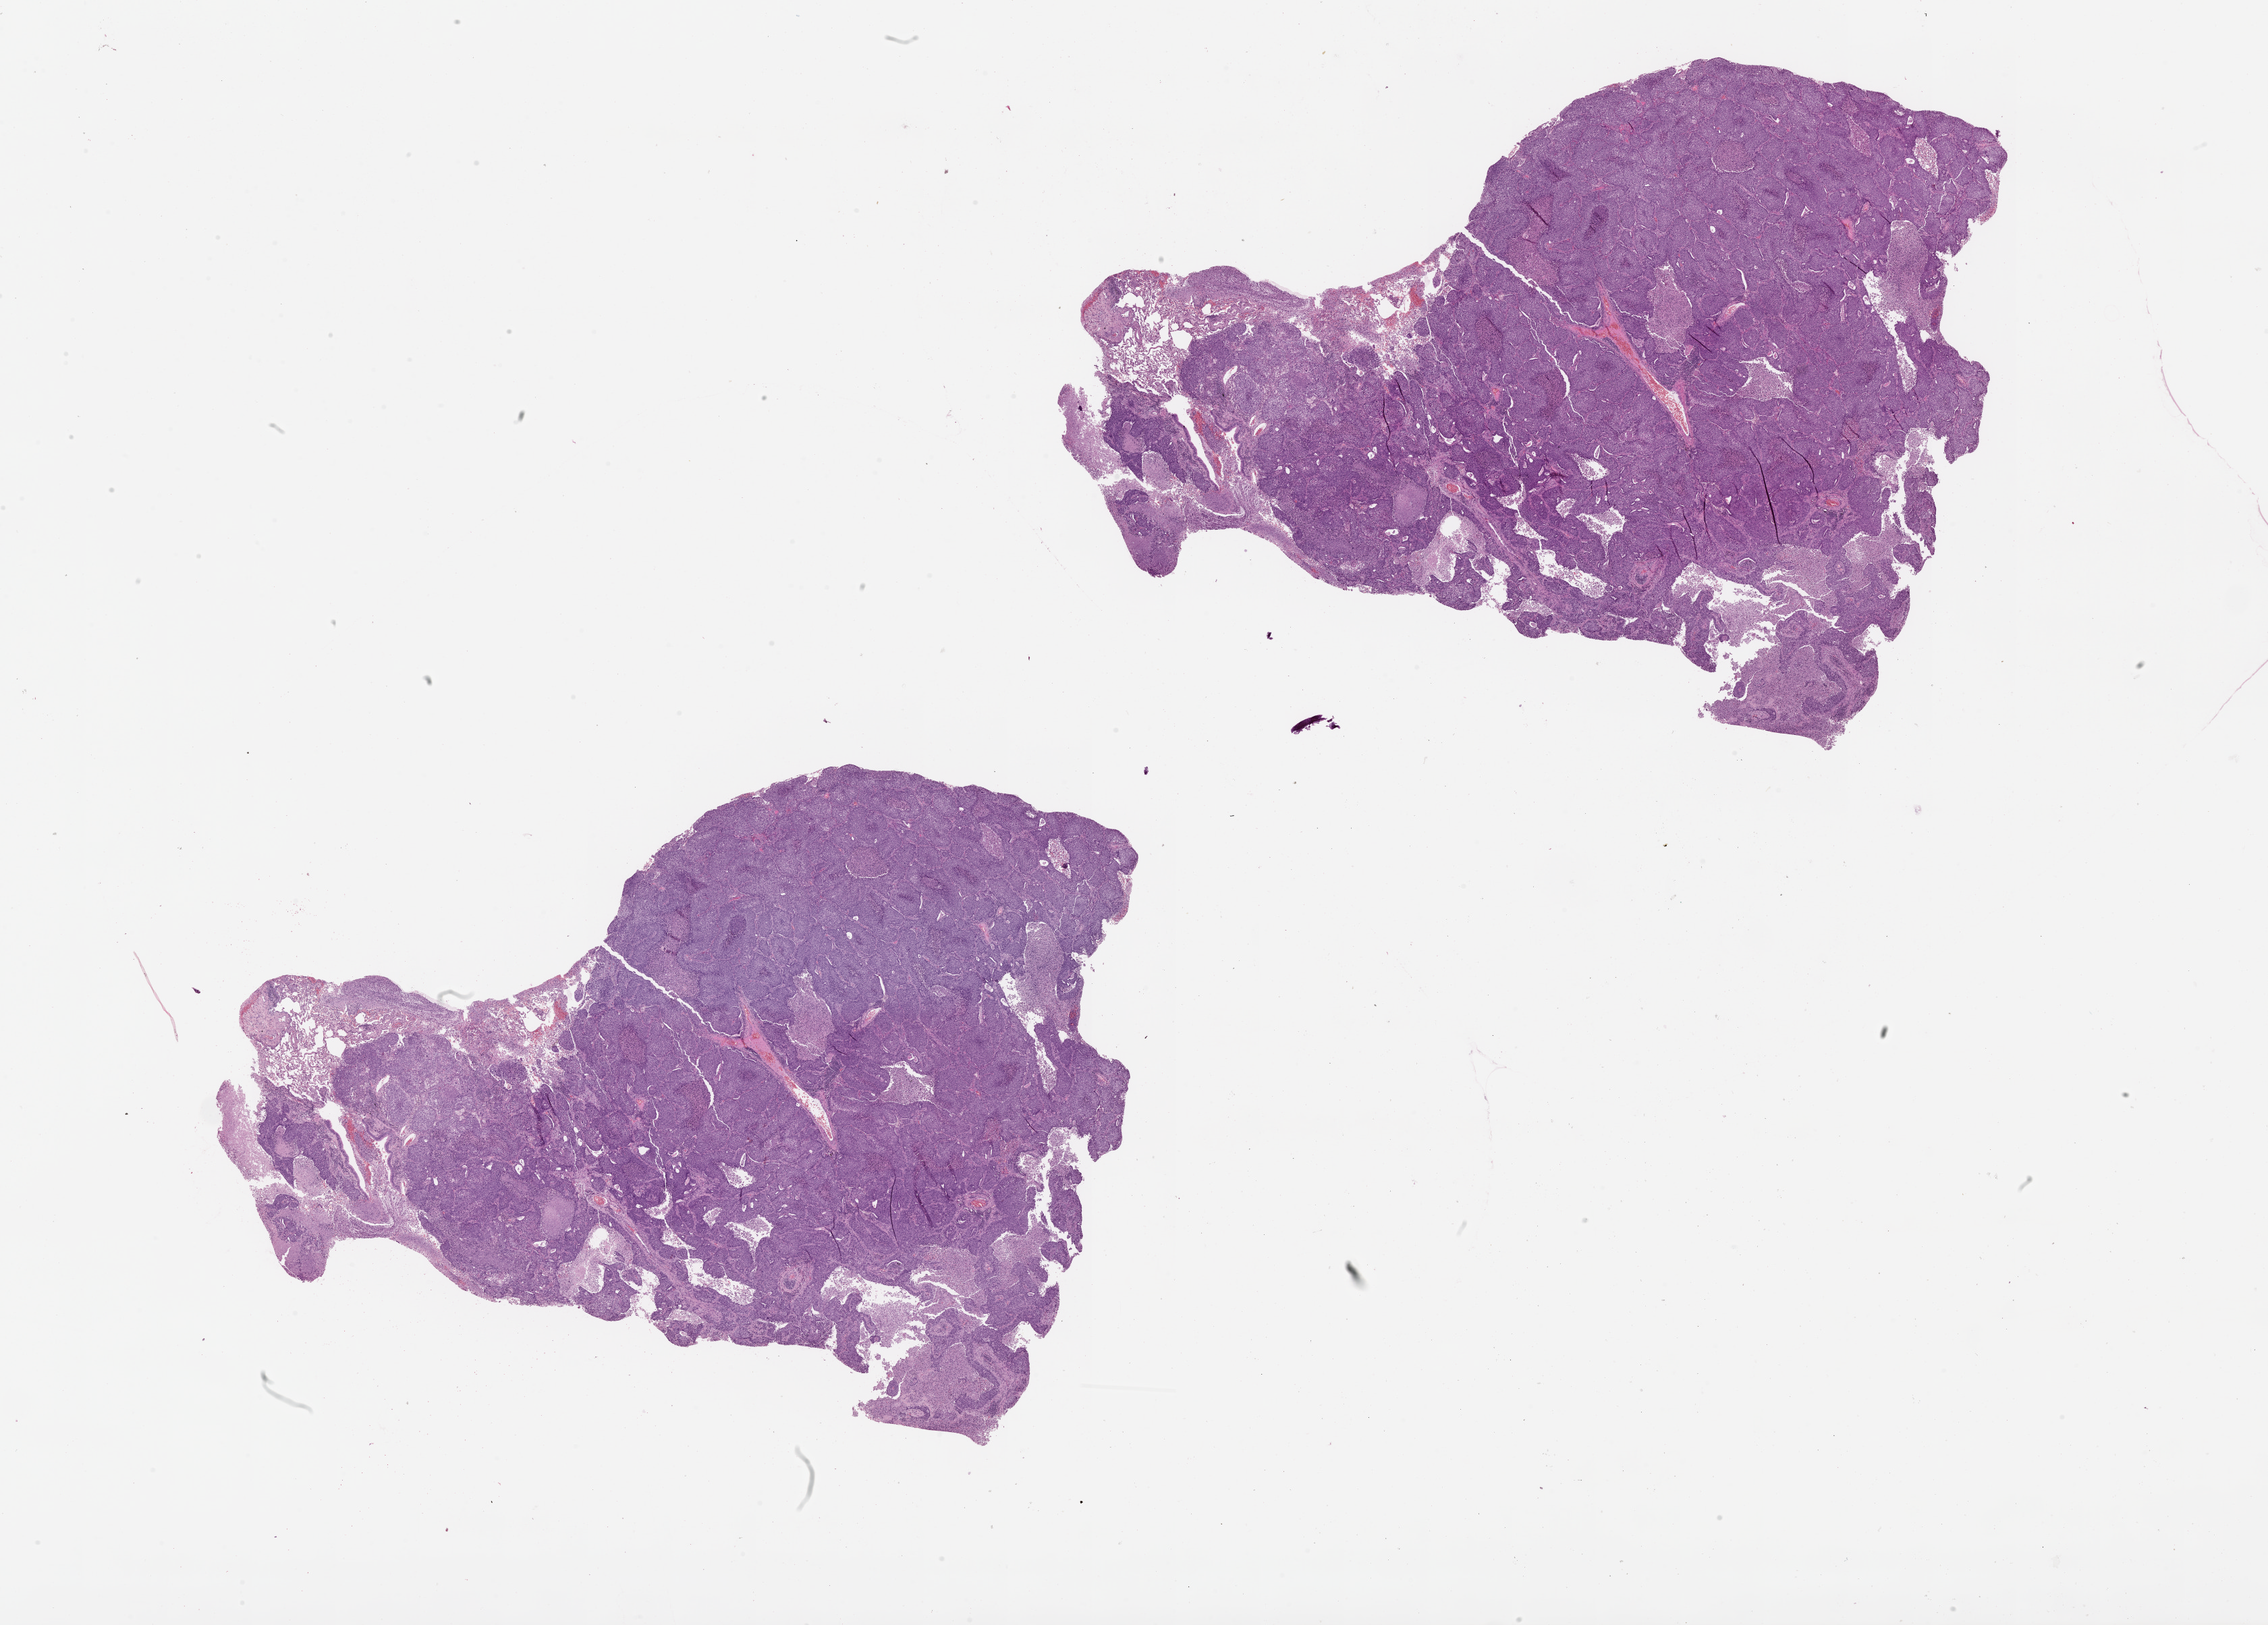
H&E-stained whole-slide image — low-resolution overview of the scanned area, about 27.1 x 19.4 mm, lung, tumour tissue. Patient: male, age 63 years.
Patient diagnosis (cohort enrolment): squamous cell carcinoma (lung).